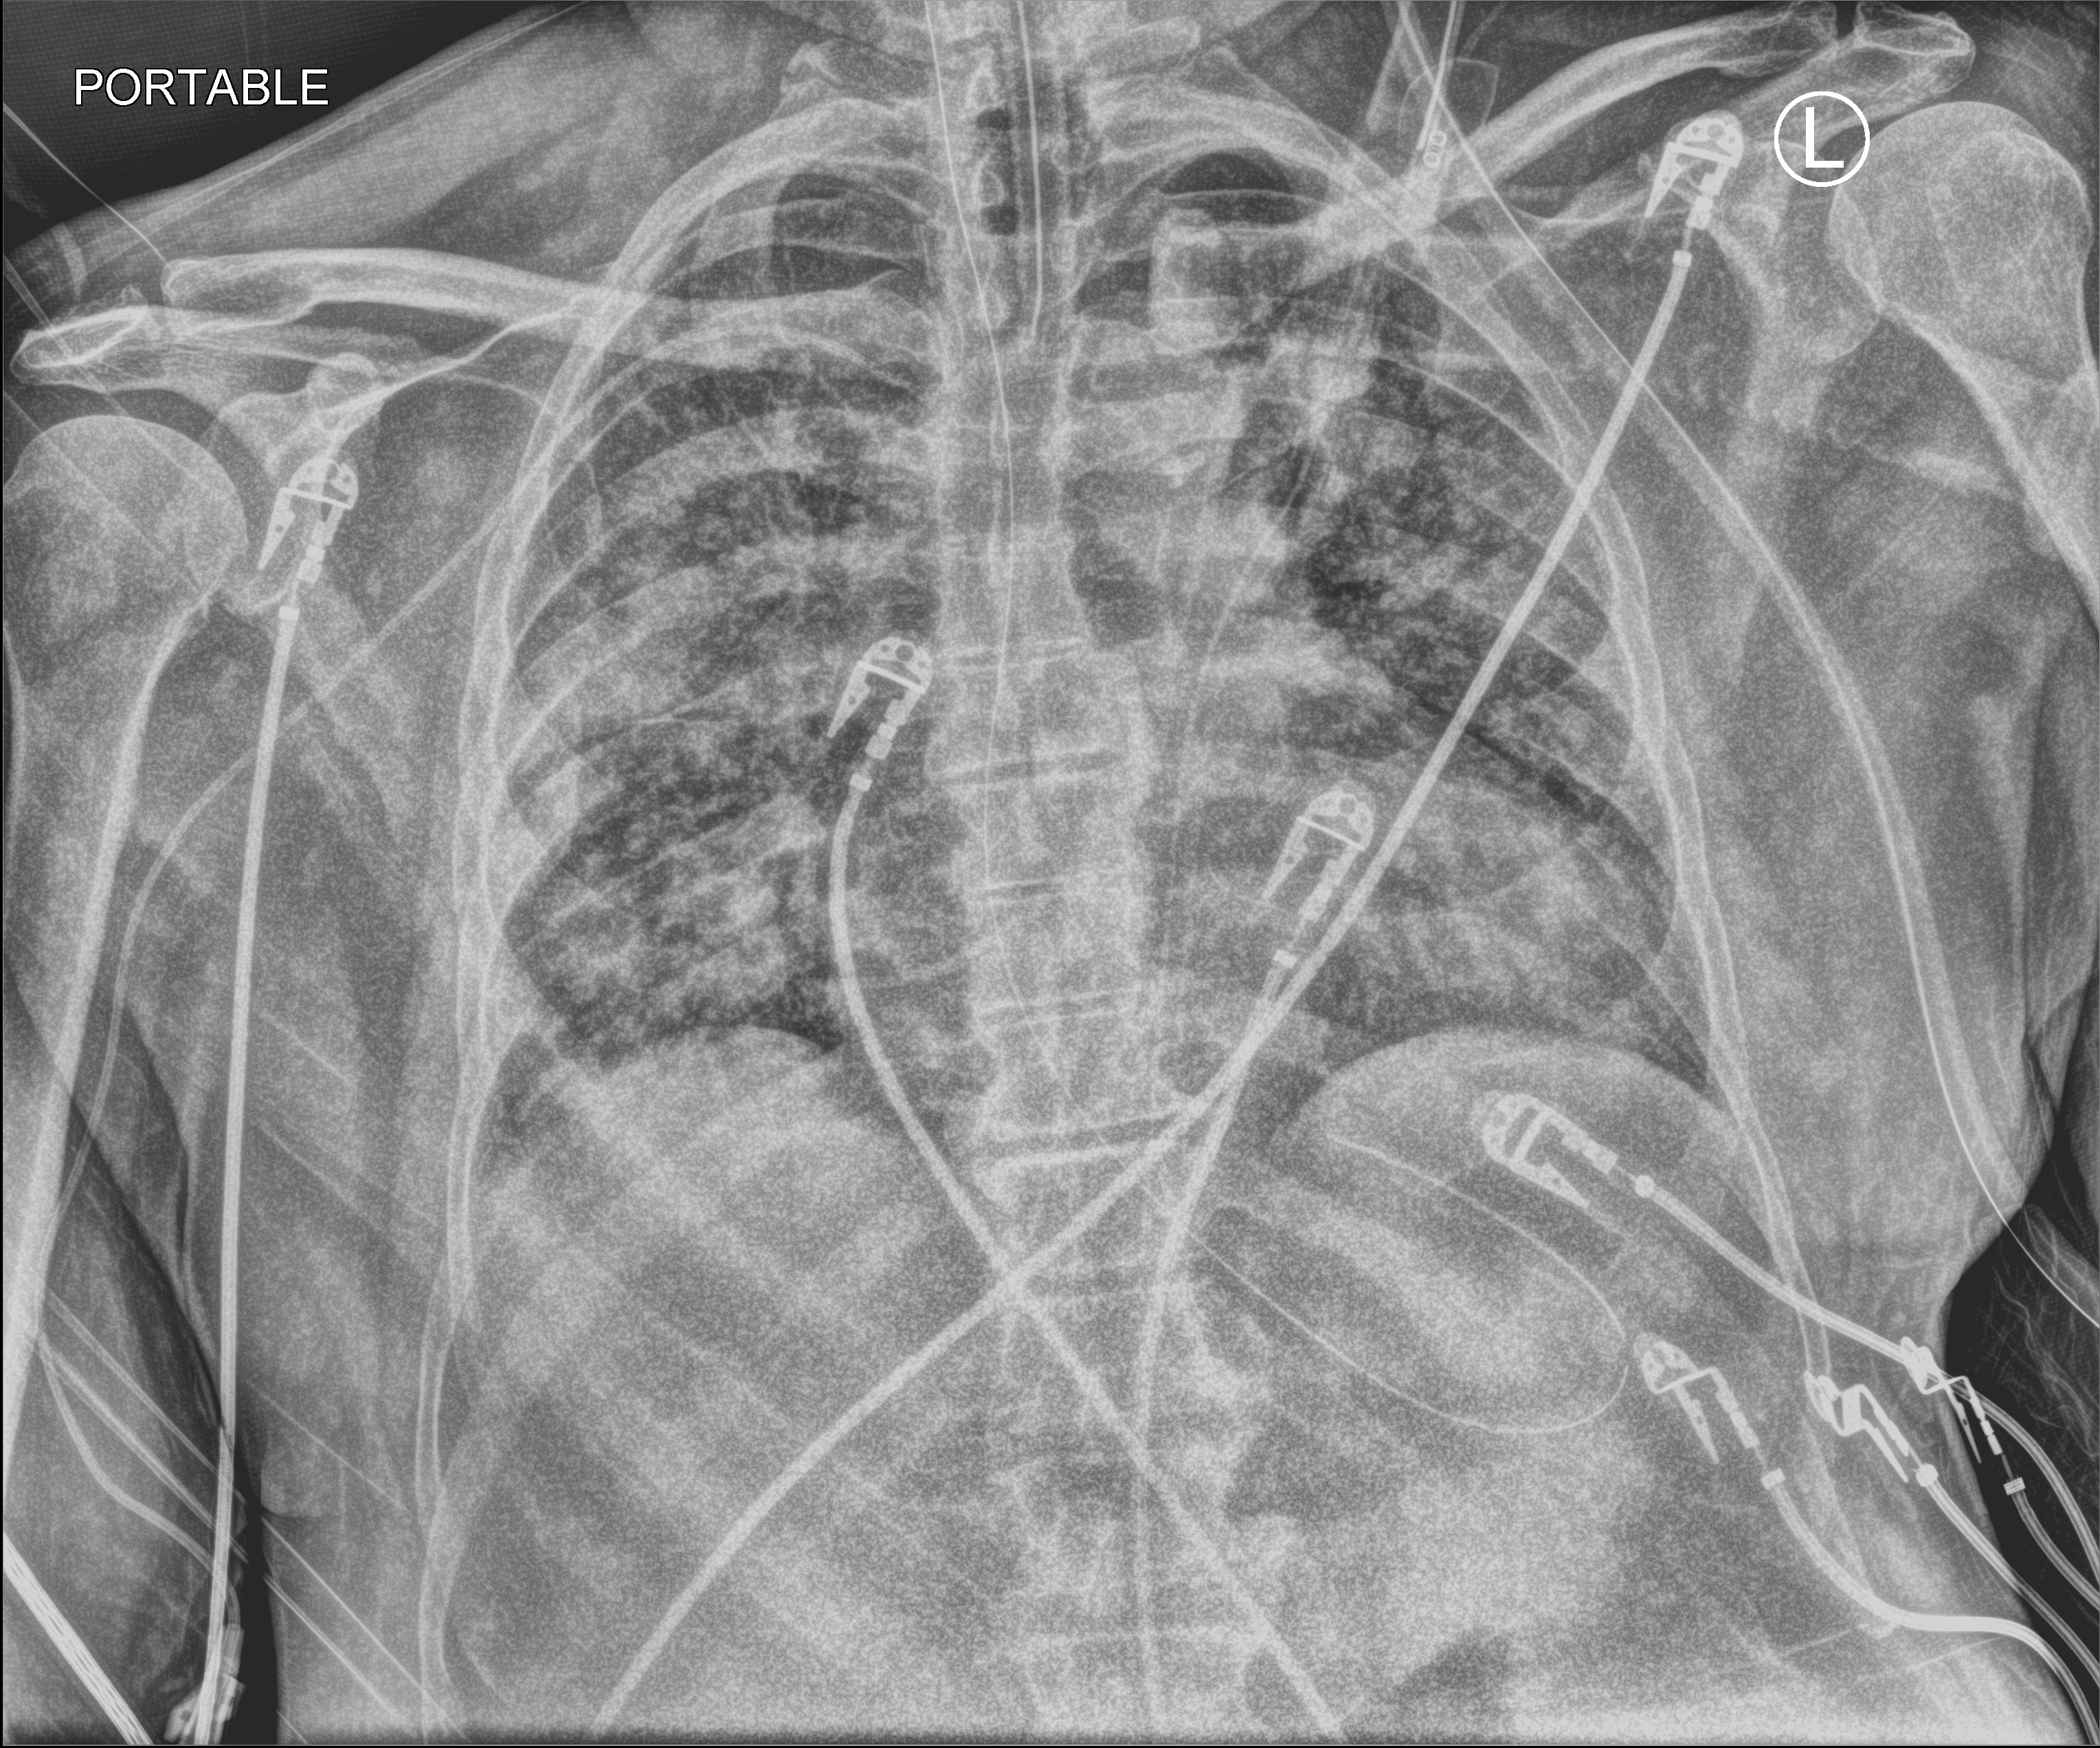
Chest X-ray (portable), anteroposterior (AP) projection. Patient hospitalised with COVID-19; male, aged 60–74 years.
Hospital-stay facts (about this admission, not read from this image; timing relative to this image not recorded): length of hospital stay: 31 days.